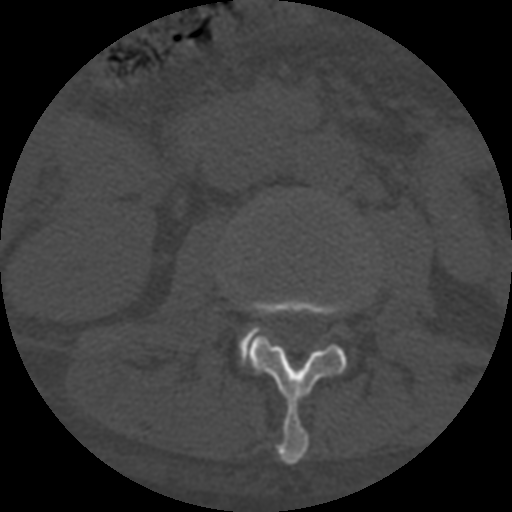
CT including the spine, one axial slice; slice 250 of 708 in the series (ordered by position); reconstruction kernel STANDARD; one of 3 acquisitions stored at this slice position; bone window (W 1800 / L 400 HU); 512 × 512 image matrix. Patient age 55 years. Case-level facts recorded for this patient, not image findings: primary cancer: colon.
Annotated regions visible in this slice (semi-automatic segmentation, software-assisted and operator-edited):
- L2 vertebra: bounding box <243,296,348,465> (left, top, right, bottom; pixels)
- L3 vertebra: <238,327,259,368>